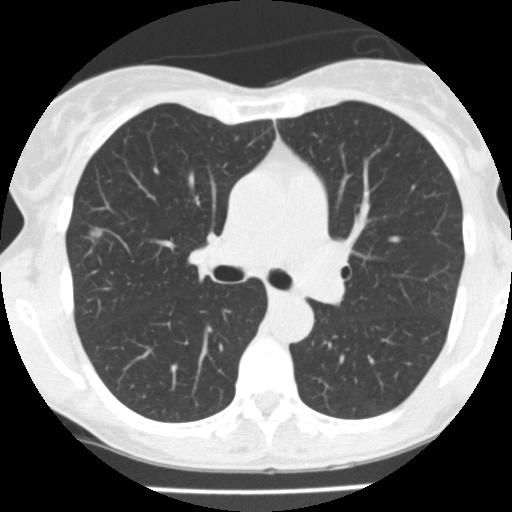
Low-dose screening chest CT, one axial slice. Position 105 of 166 along the scan axis. Reconstruction kernel FC10. Lung window (W 1500 / L -600 HU). 2 mm slice thickness. 512 × 512 image matrix.
Annotated regions visible in this slice (expert manual segmentation):
- lesion 1 (tumor, upper lobe of right lung): box from (x=91, y=228) to (x=102, y=237) px